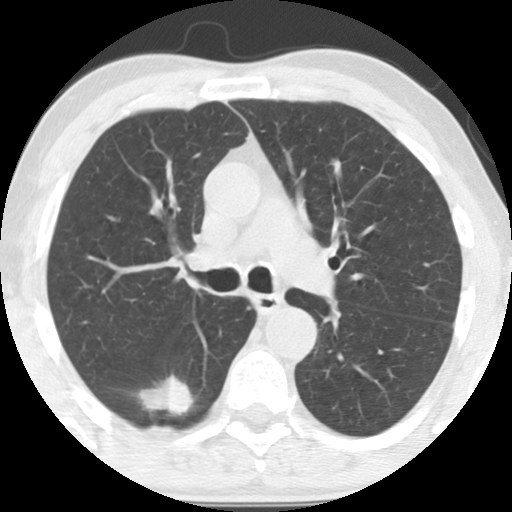
Low-dose screening chest CT, one axial slice. Slice 90 of 135 in the series (ordered by position). 120 kVp. Lung window (W 1500 / L -600 HU). 2.5 mm slice thickness. 512 × 512 image matrix, field of view 300 × 300 mm.
Structures marked on this image (manually delineated by an expert):
- lesion 1 (tumor, lower lobe of right lung): bounding box <138,376,194,416> (left, top, right, bottom; pixels)